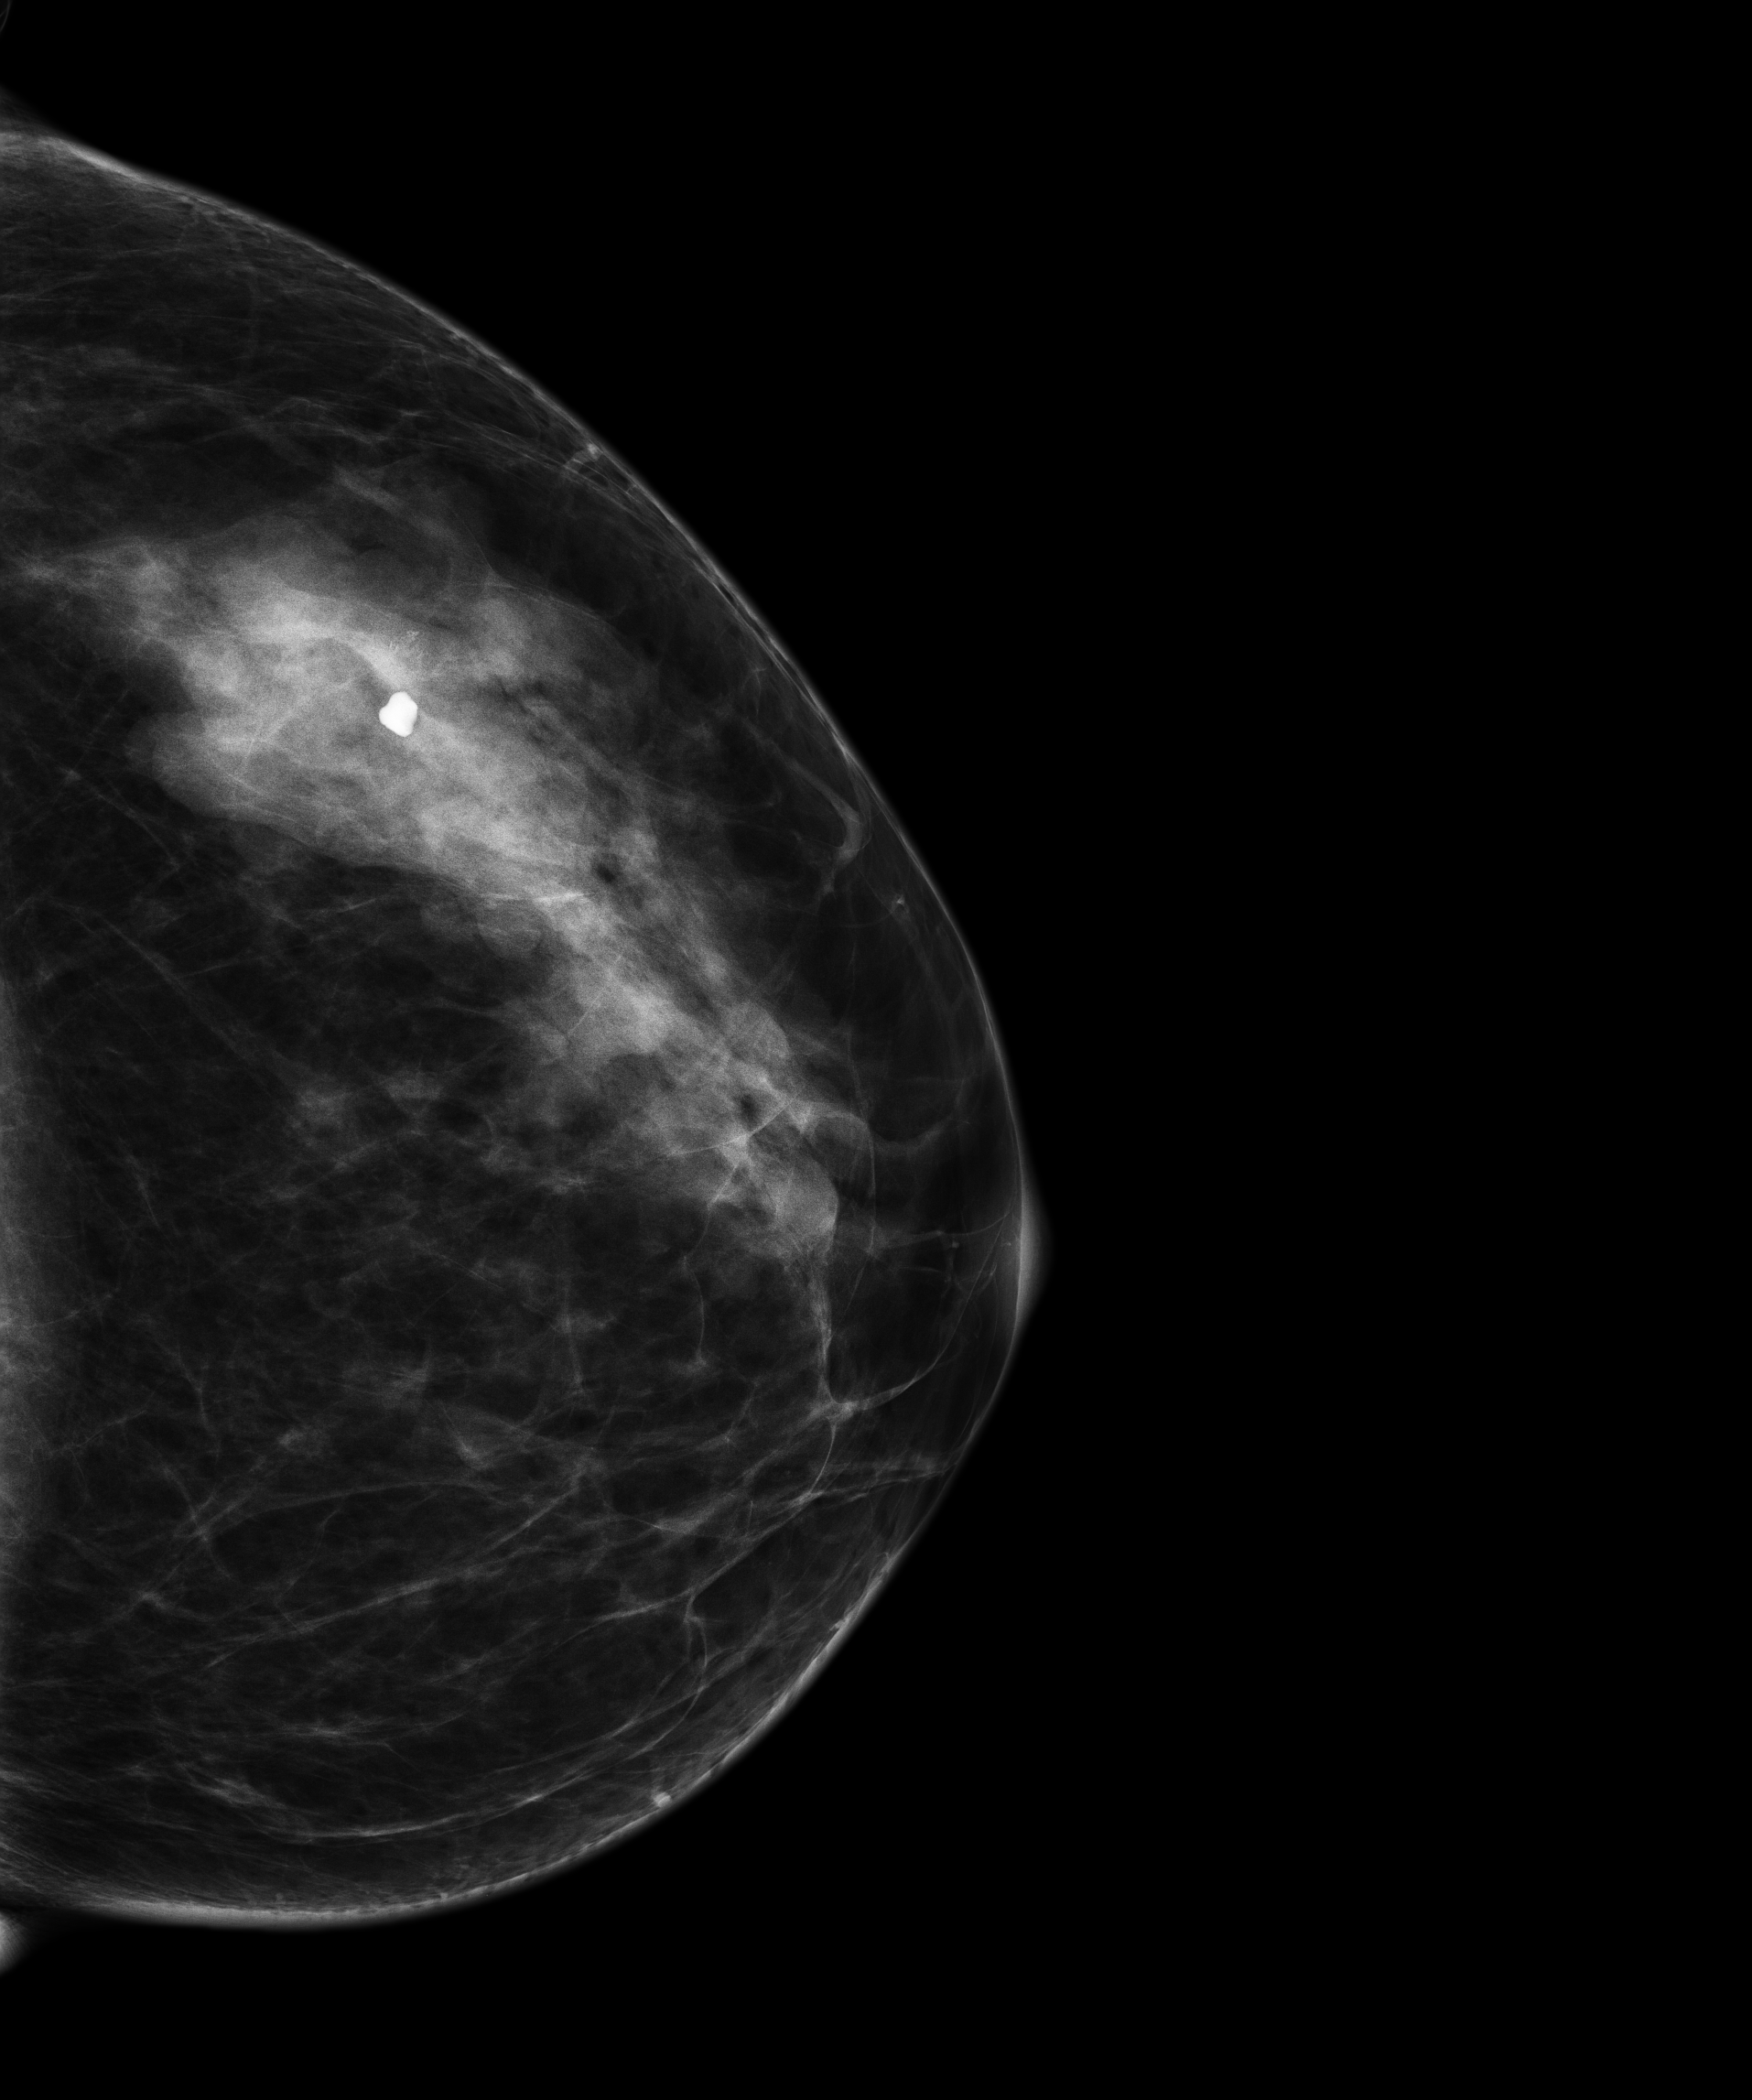
Digital mammogram (FFDM), left breast, craniocaudal (CC) view, annual screening mammography examination. Female patient, age 51 years.
Final BI-RADS assessment for this screening round (tomosynthesis exam, both breasts): category 2.